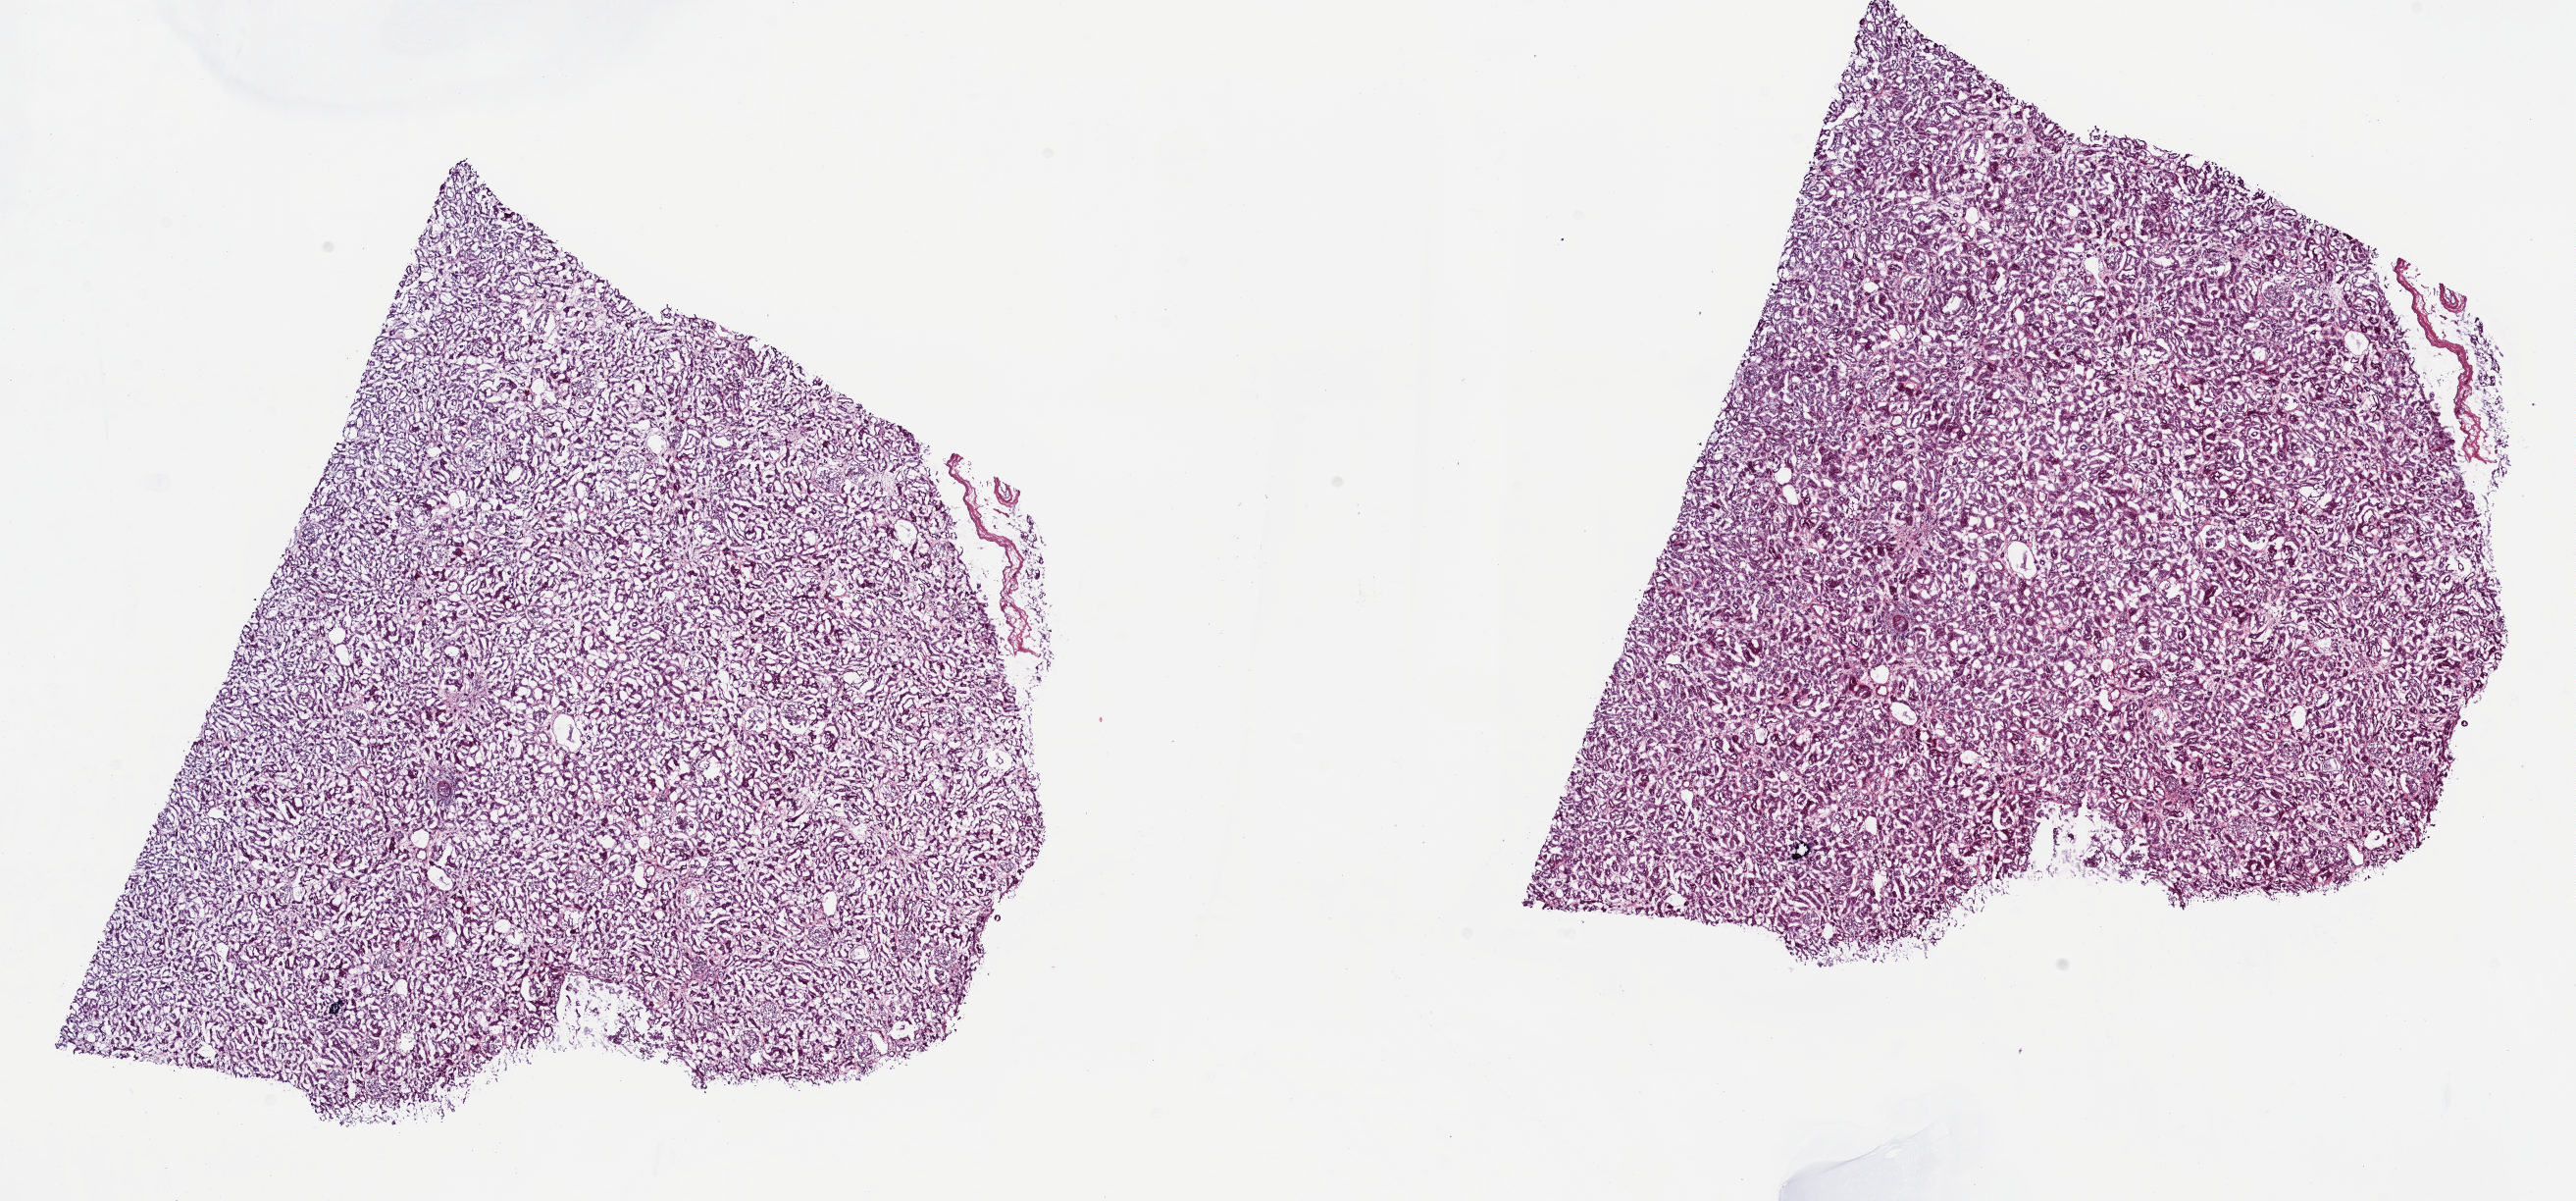
Digitized H&E-stained tissue section (whole slide), whole scanned area (about 20.8 x 9.7 mm) shown as a low-resolution overview, frozen section from the top of the tissue portion, solid tissue normal (non-tumour tissue) sample from the retroperitoneum and peritoneum. Female, age 53 years at initial diagnosis. Pathologist review of this section (percent, as recorded): tumour cells 0%, tumour nuclei 0%, normal cells 50%, stromal cells 50%, necrosis 0%. Infiltration values recorded for this section: lymphocyte infiltration 3%, monocyte infiltration 1%, neutrophil infiltration 2%.
- this section: solid tissue normal sample (biorepository sample class)
- patient diagnosis: Leiomyosarcoma, NOS (retroperitoneum)